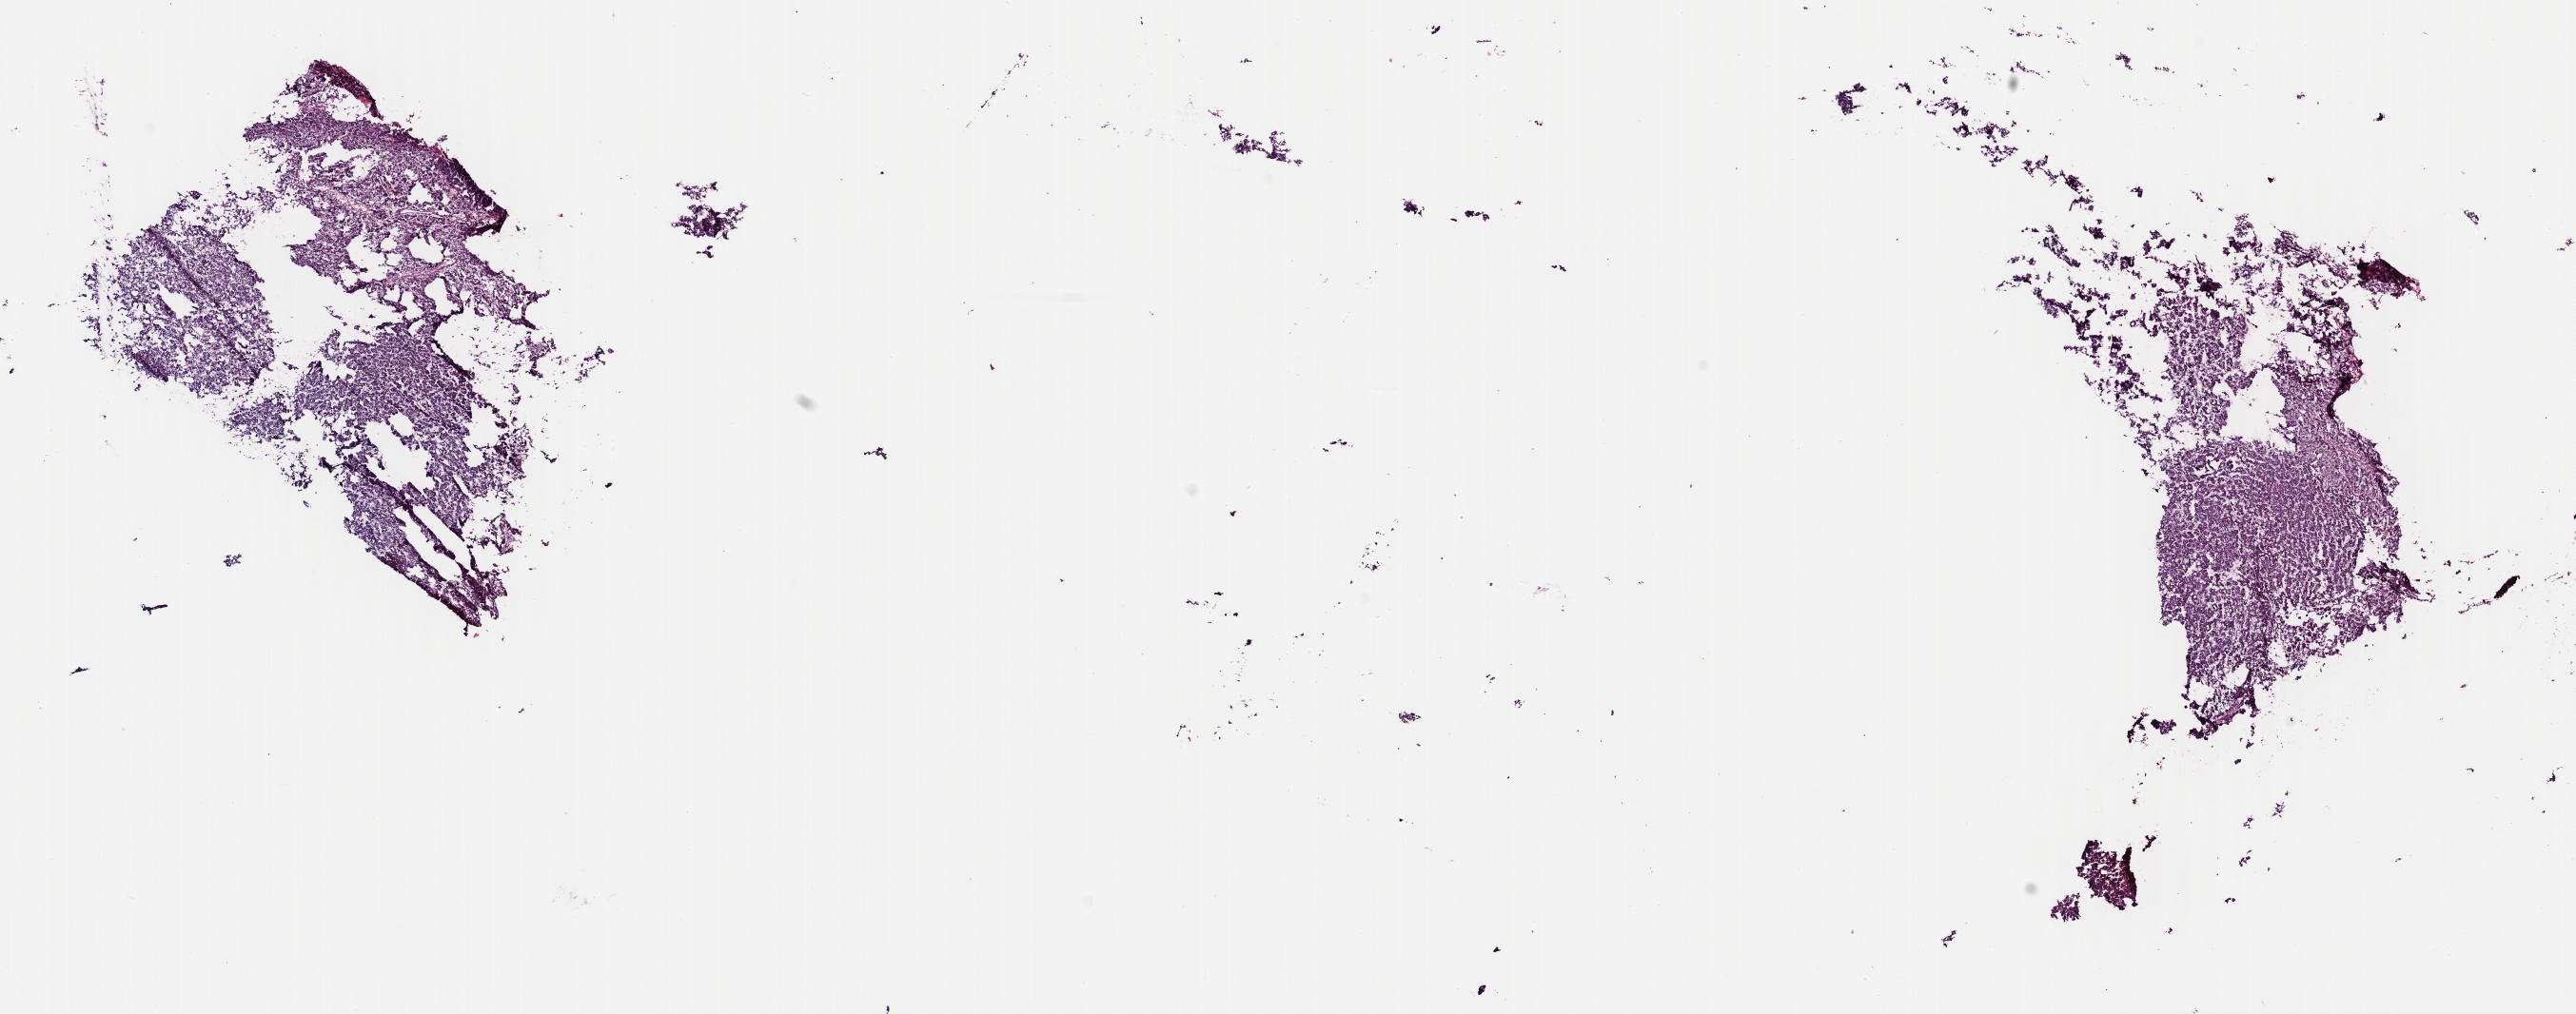
Whole-slide histology image, H&E-stained, shown as a low-resolution overview of the whole scanned area (about 21.4 x 8.4 mm); frozen section; sample: primary tumour, liver. Male, age 71 years at initial diagnosis.
Pathologic diagnosis: Hepatocellular carcinoma, NOS.